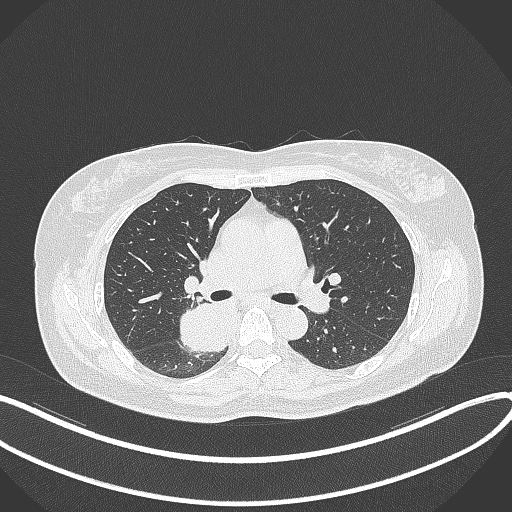
Chest CT, one axial slice; slice 220 of 331 in the series (ordered by position); reconstruction kernel B70f; 120 kVp; lung window (W 1500 / L -600 HU); 1 mm slice thickness; 512 × 512 image matrix, field of view 400 × 400 mm. Patient: female, 54 years. Case-level facts recorded for this patient, not image findings: clinical TNM (as recorded): T4 N0 M0.
Outlined on this slice (bounding box drawn by a radiologist):
- lung tumour (recorded histology: adenocarcinoma): box from (x=173, y=298) to (x=239, y=354) px